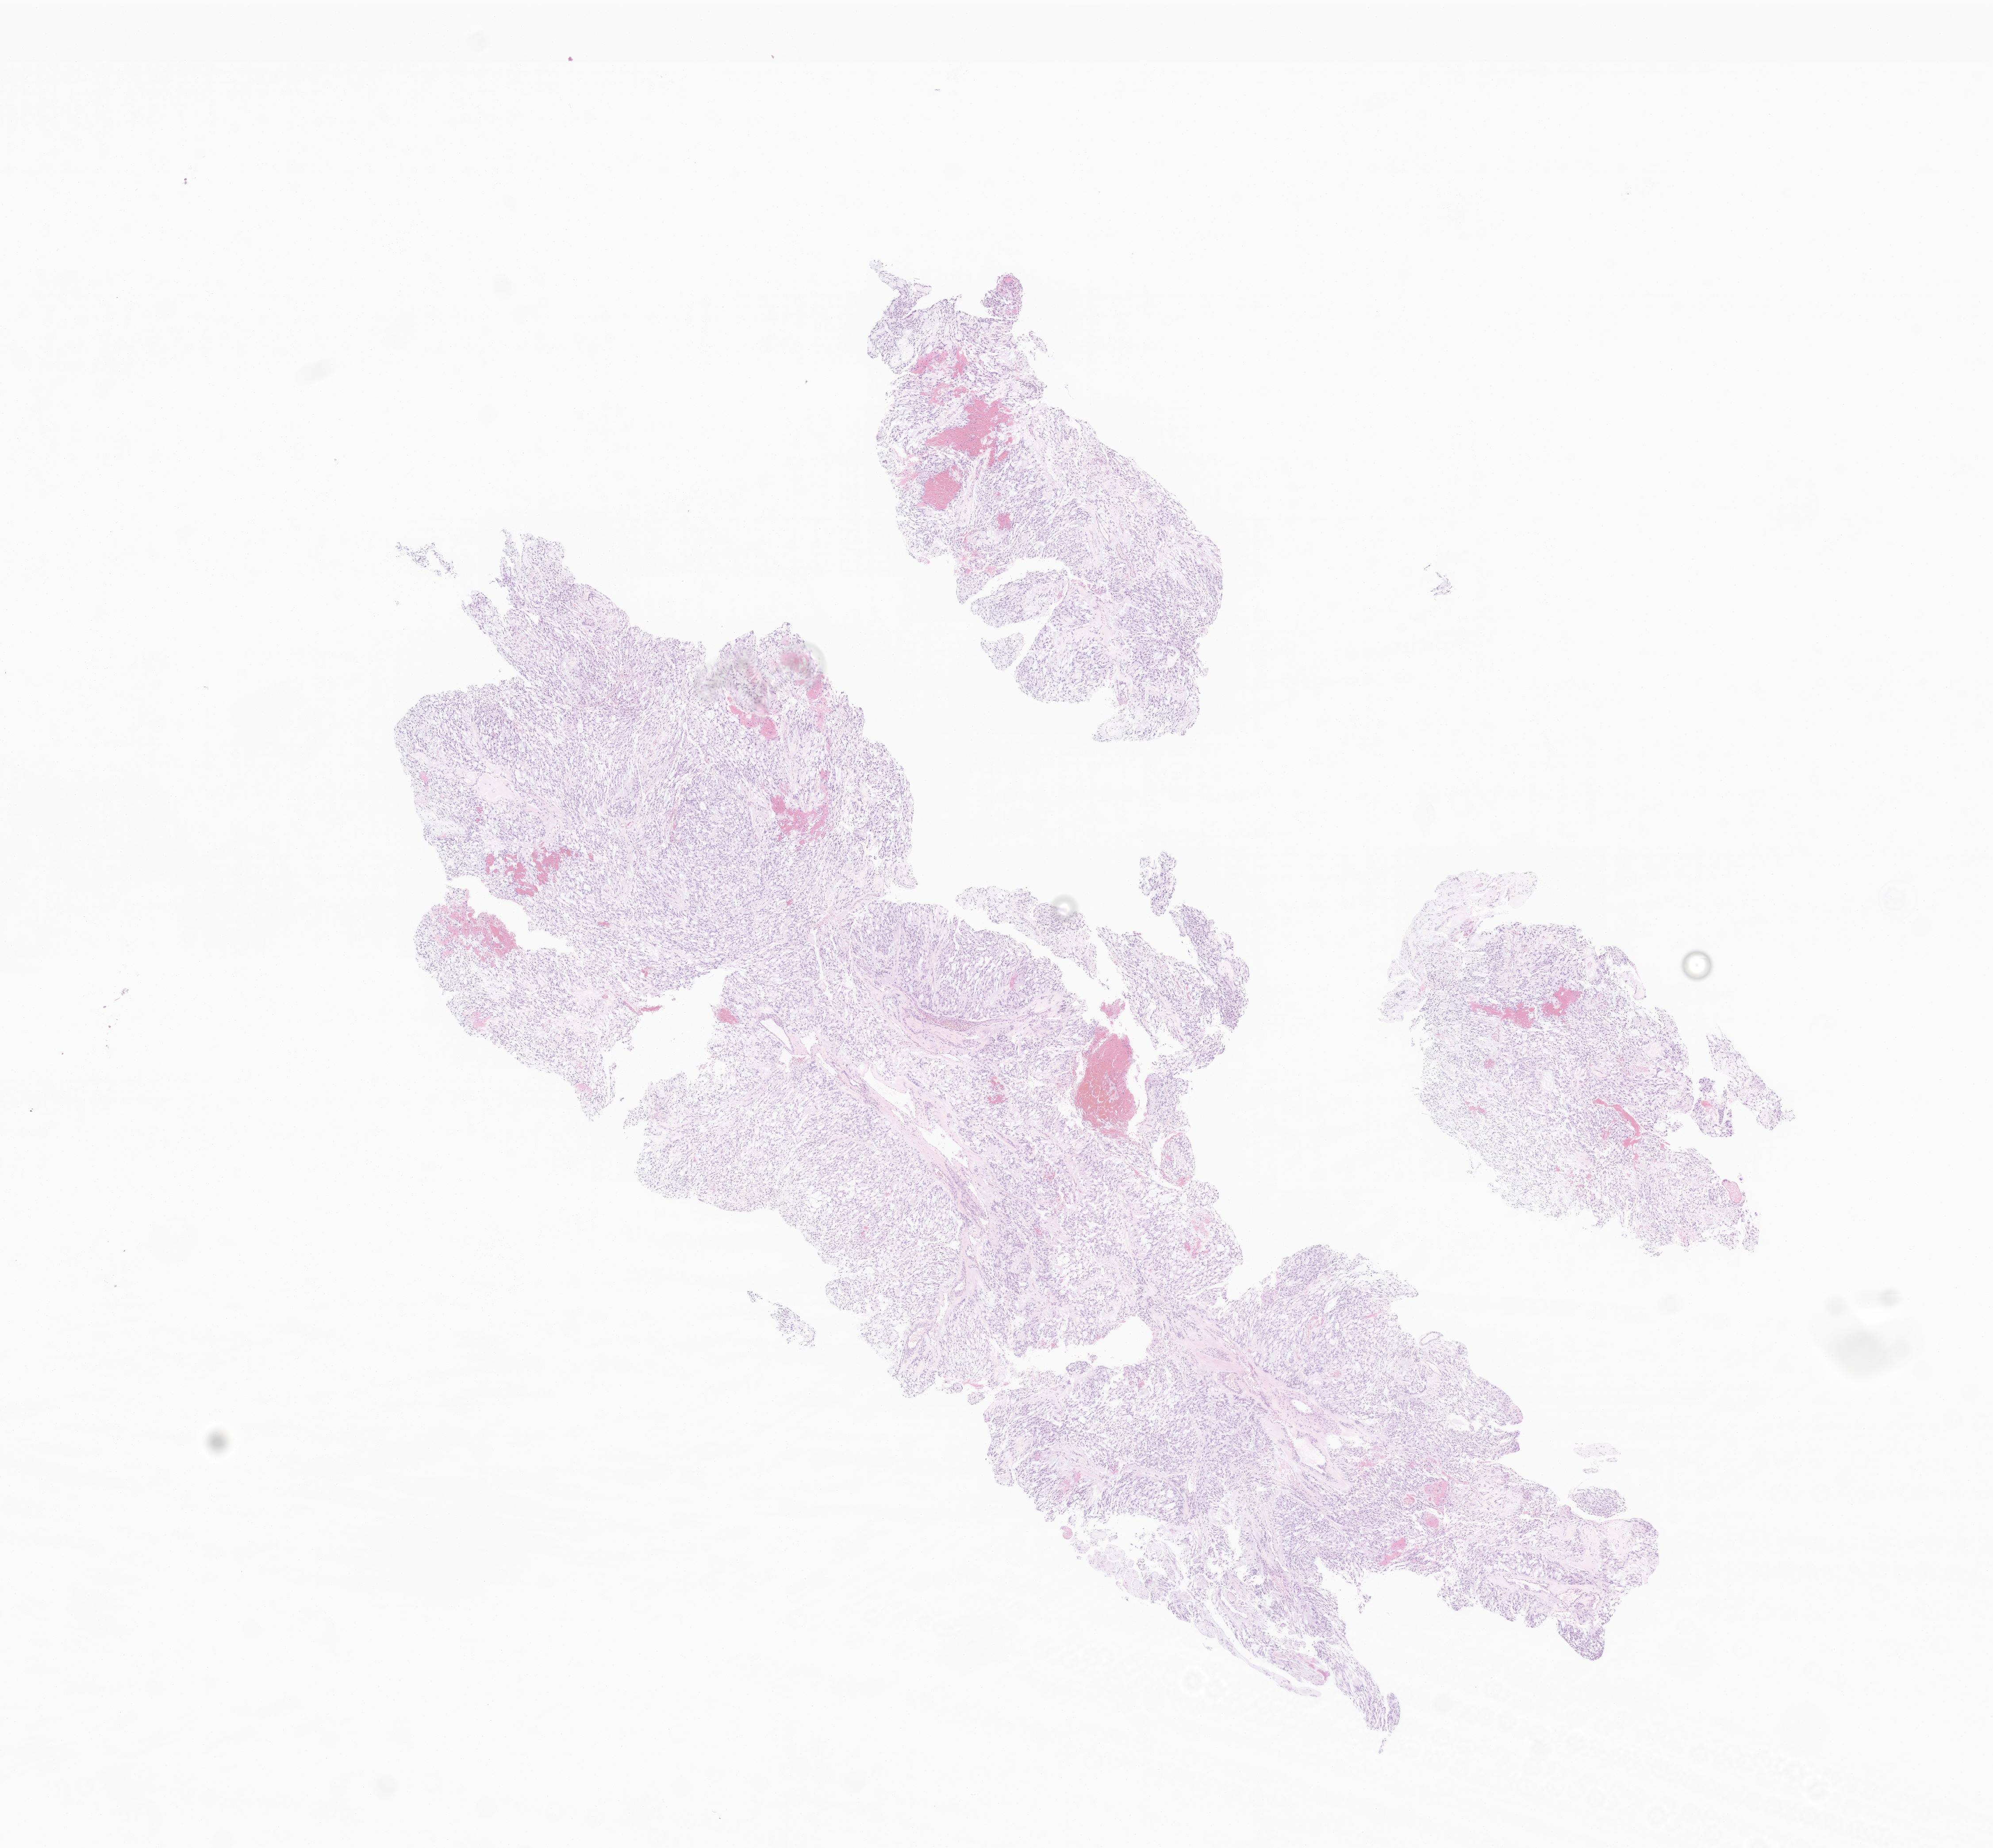
H&E whole-slide image of tumor tissue from the spinal cord — low-resolution overview of the scanned area, about 19.0 x 17.6 mm. Formalin-fixed paraffin-embedded section. Female patient, age 112 months (9 years 4 months).
Diagnosis: Myxopapillary ependymoma.